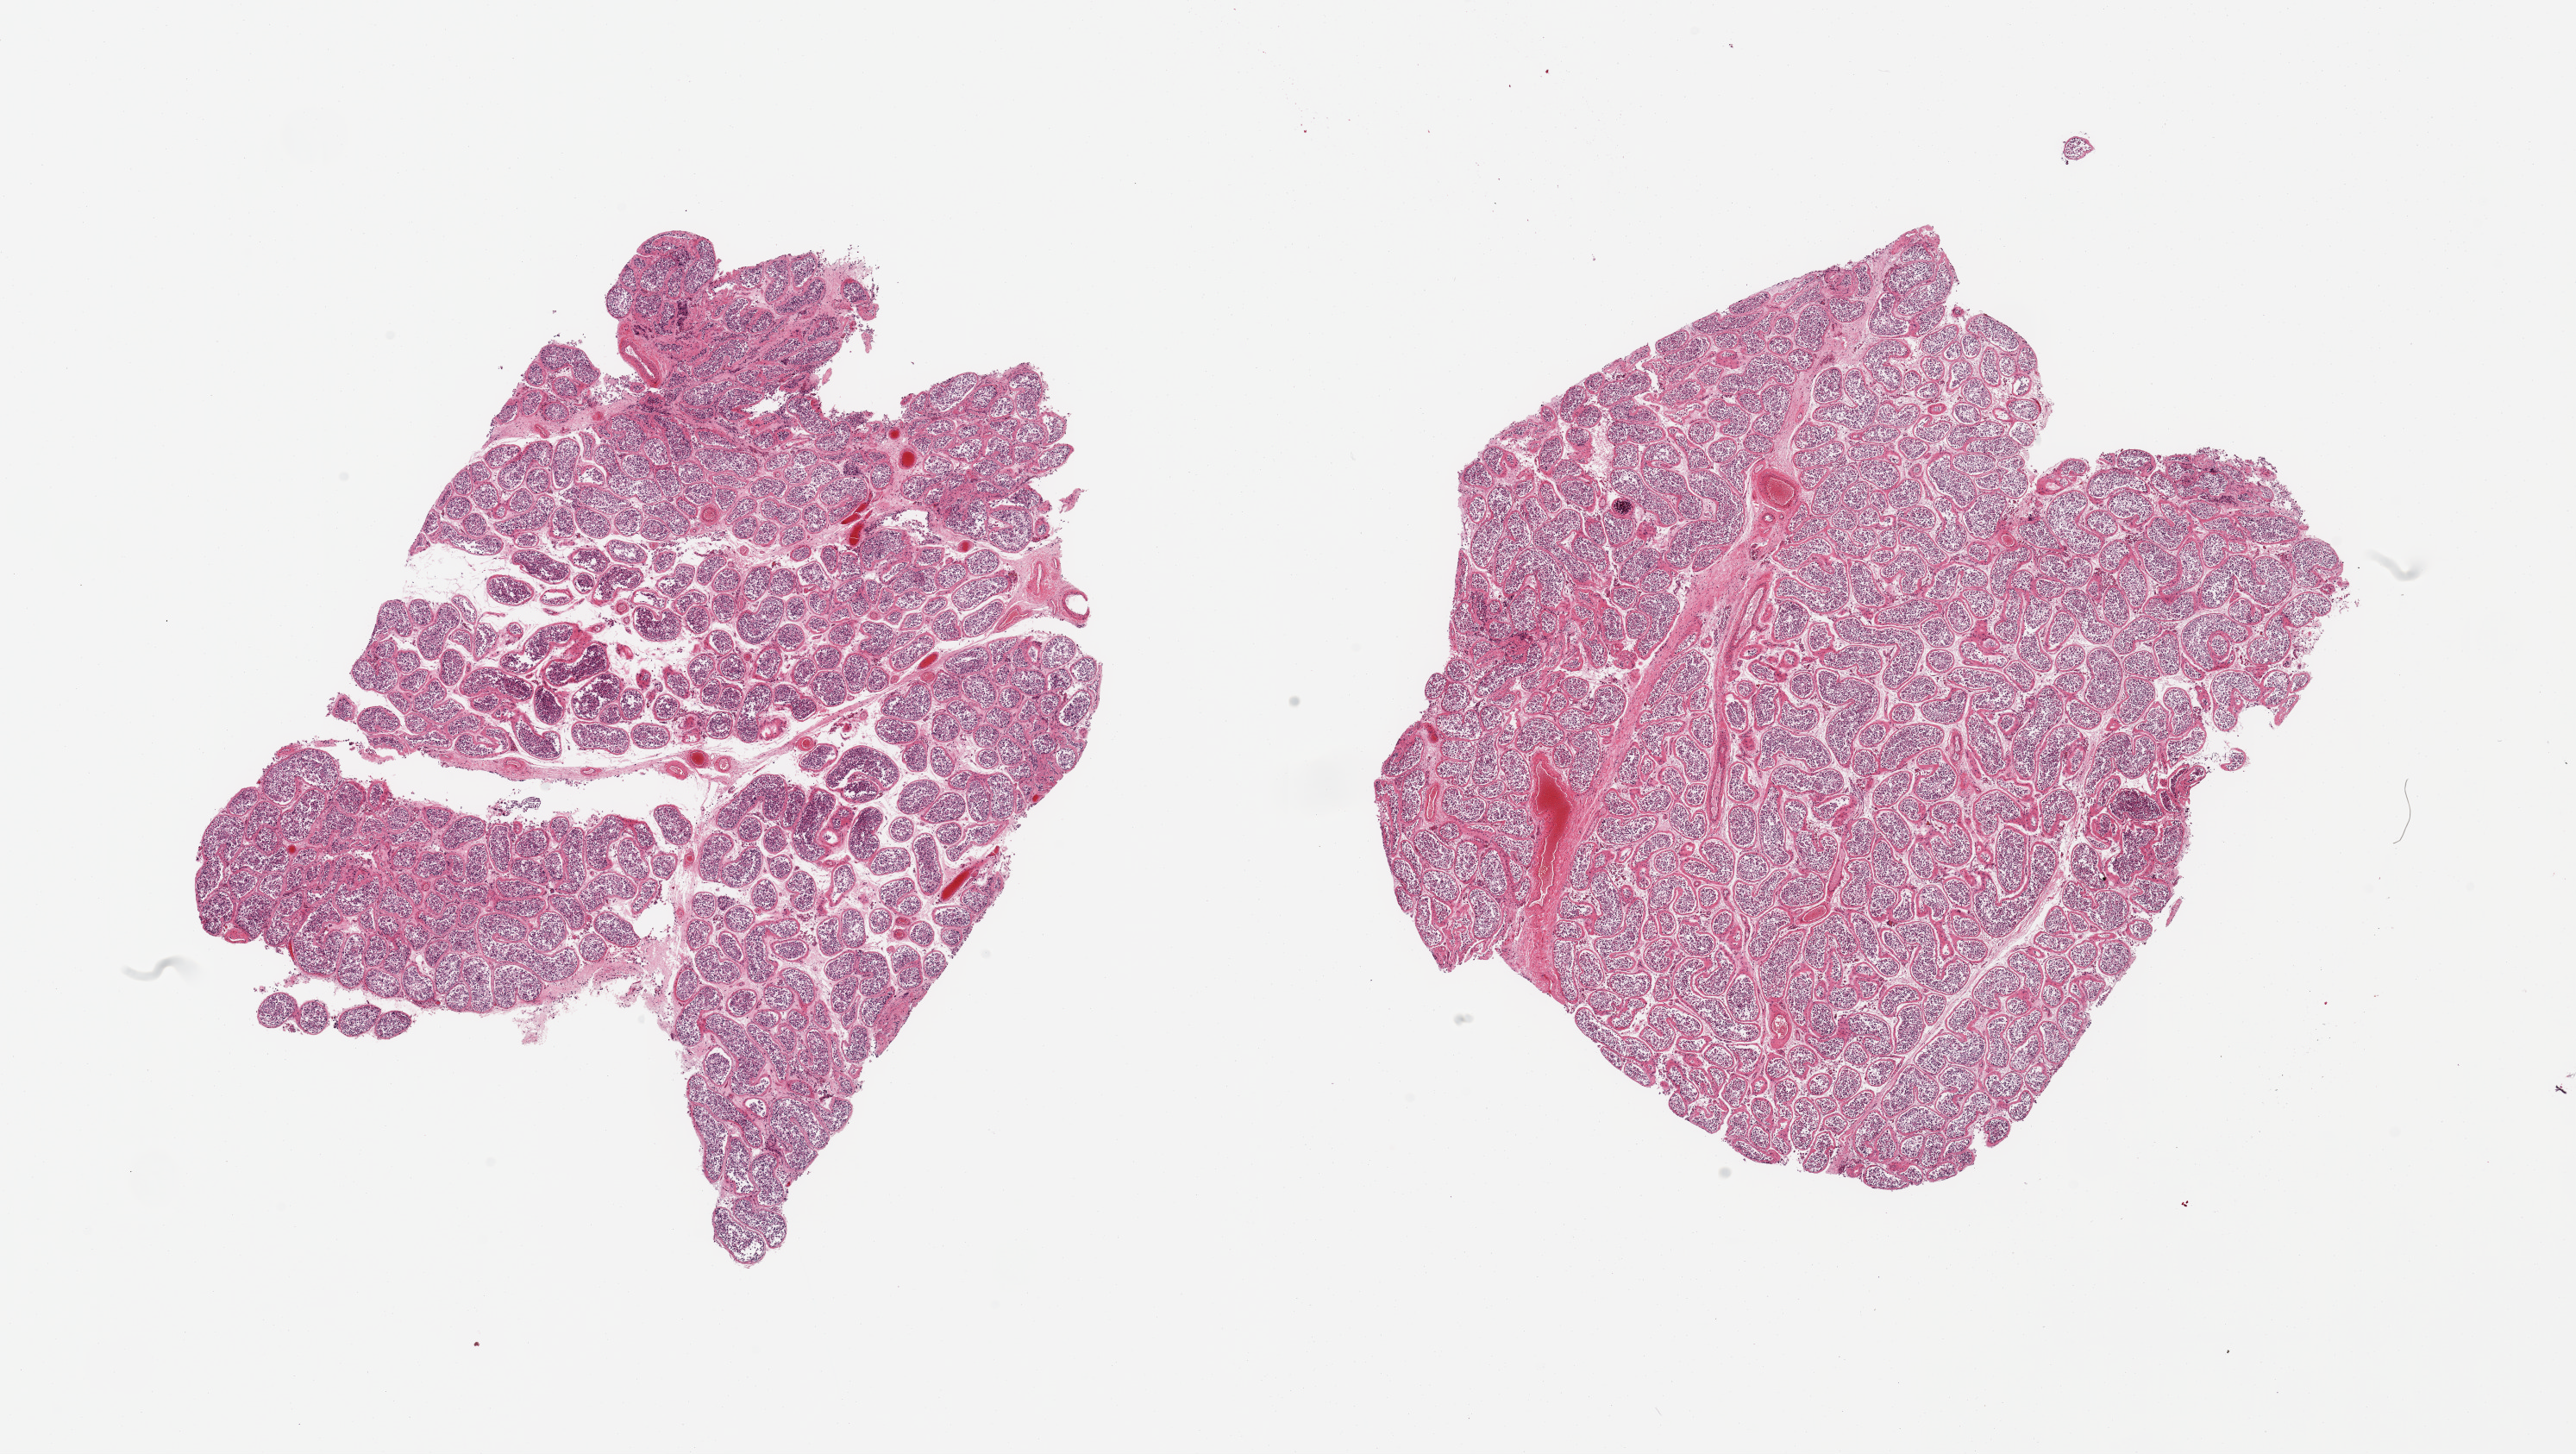
Whole-slide image, hematoxylin and eosin (H&E) stain — a low-resolution overview of the entire scanned area, about 23.6 x 13.3 mm. PAXgene-fixed paraffin-embedded (PFPE) section. Section of testis (target tissue). Donor tissue sample.
- review note (as recorded): 2 pieces; active spermatogenesis